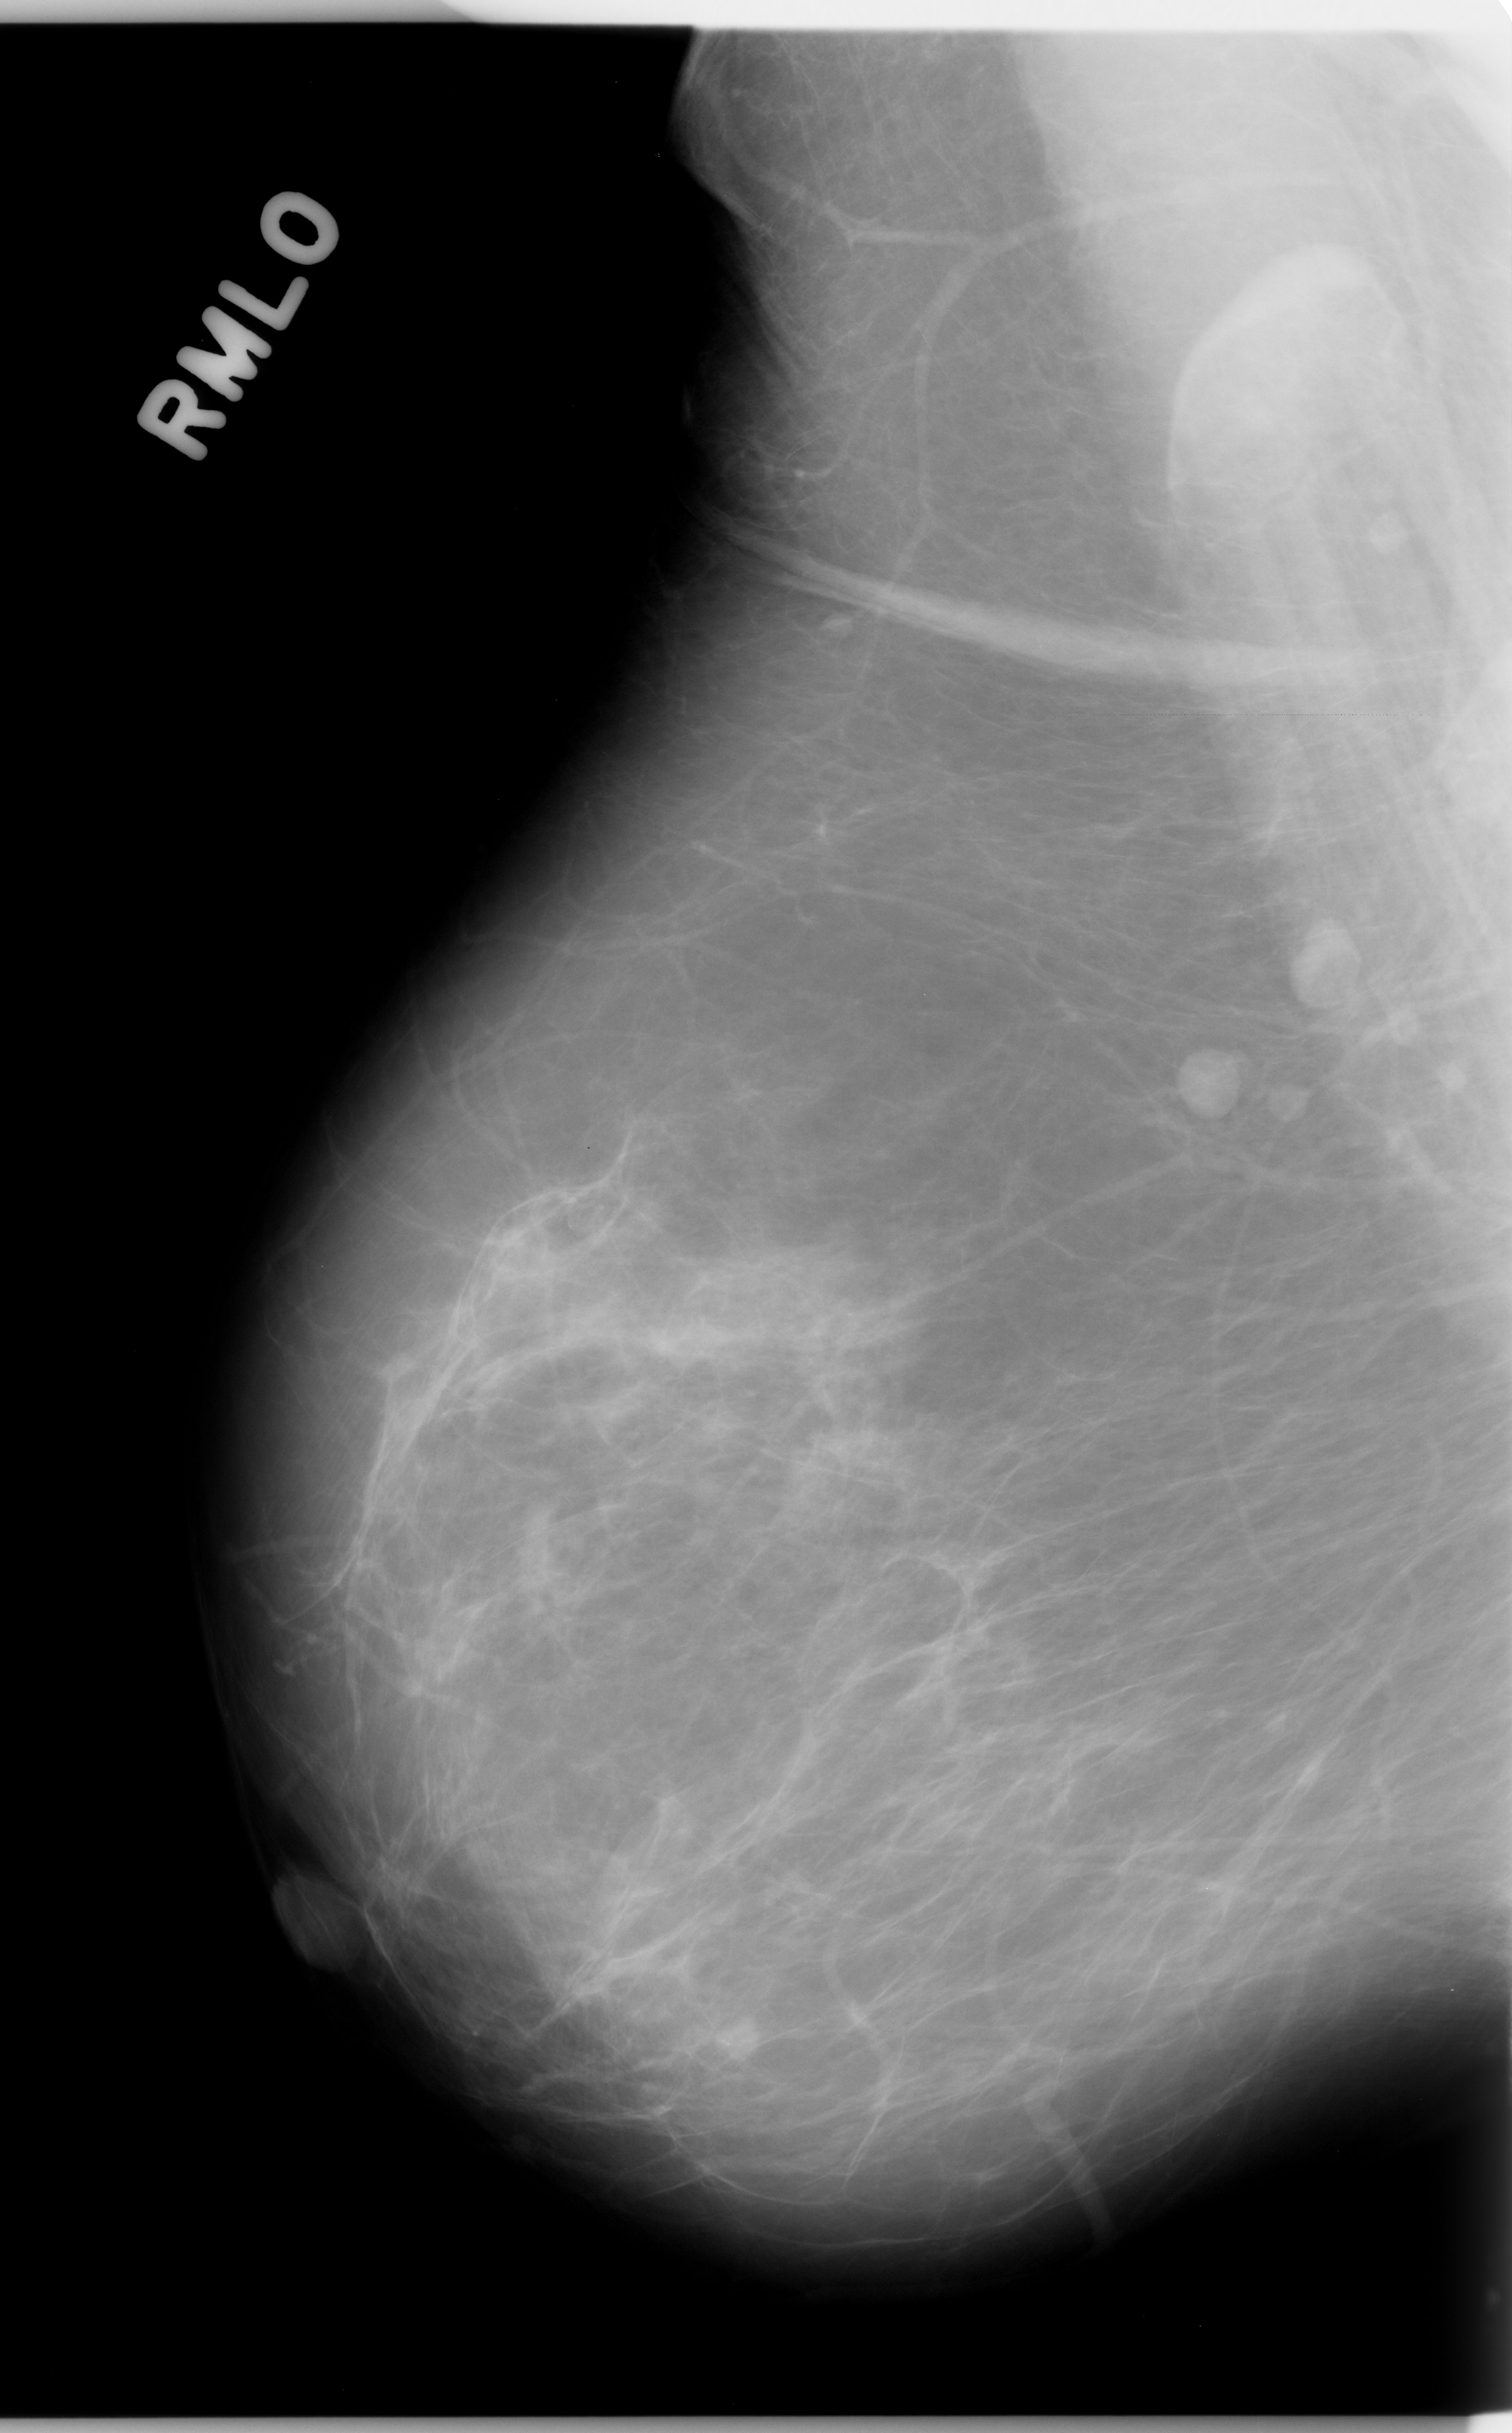
Digitized screen-film mammogram; right breast; mediolateral oblique (MLO) view; BI-RADS breast density category 1 (scale 1–4).
- Abnormality record for this image: calcifications, morphology punctate, distribution clustered; BI-RADS assessment category 4; subtlety rating 5 on a 1 (subtle) to 5 (obvious) scale; pathology result (as recorded, not read from the image): benign.